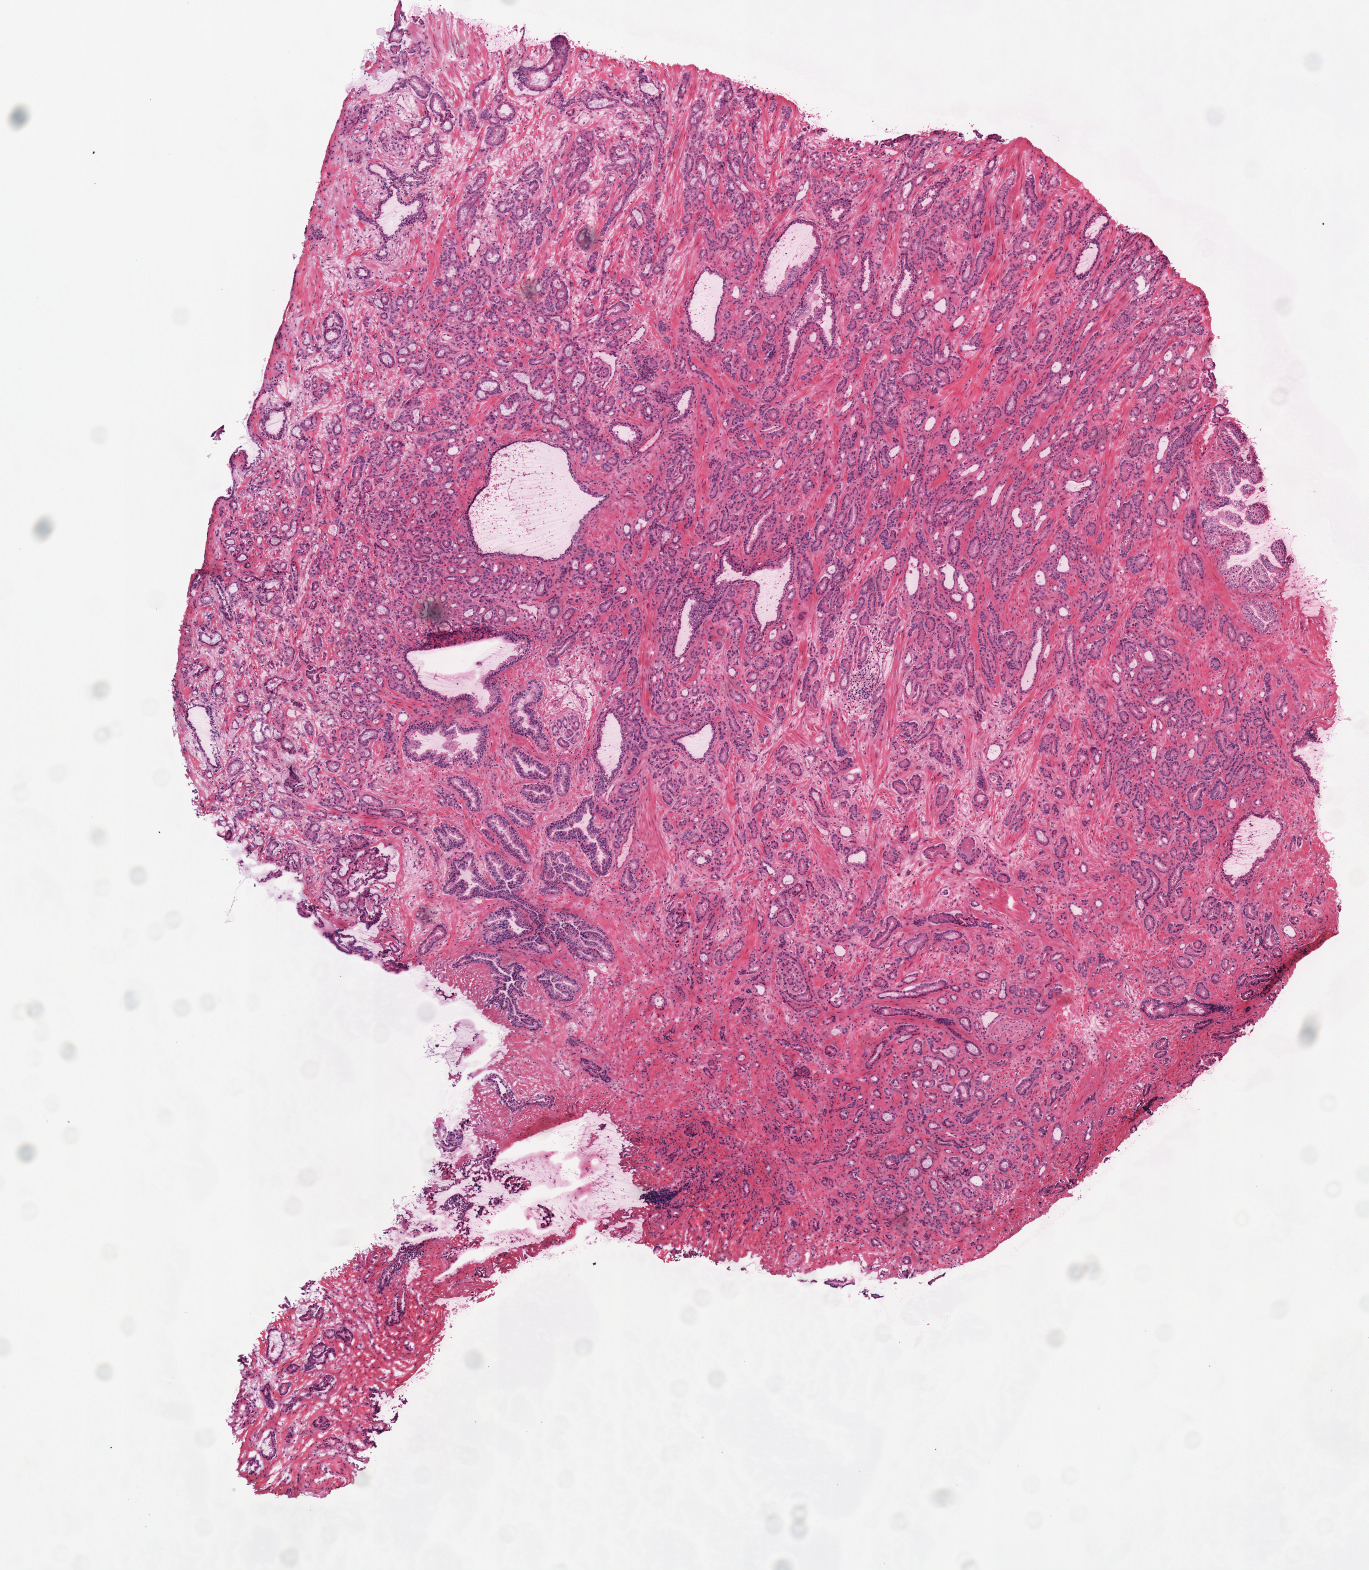
Whole-slide histology image, H&E — whole scanned area (about 5.4 x 6.2 mm) shown as a low-resolution overview, frozen section from the top of the tissue portion, sample: primary tumour, prostate. Male patient; age at initial diagnosis 49 years.
Diagnosis: Acinar cell carcinoma (prostate gland).